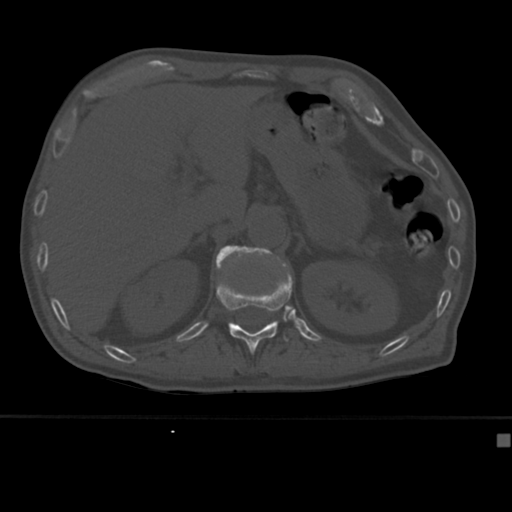
CT including the spine, one axial slice. Position 187 of 430 along the scan axis. Reconstruction kernel Br40s. Bone window (W 1800 / L 400 HU). 1.5 mm slice thickness. 512 × 512 image matrix. Patient: male, 64 years. Case-level facts recorded for this patient, not image findings: primary cancer: uterus; vertebrae with lytic lesions (as recorded): T1, T4, T5, T7, L5.
Outlined on this slice (semi-automatically segmented with operator editing):
- L1 vertebra: bounding box (x1, y1, x2, y2) in pixels: (216, 245, 281, 271)
- T12 vertebra: (216, 276, 293, 354)